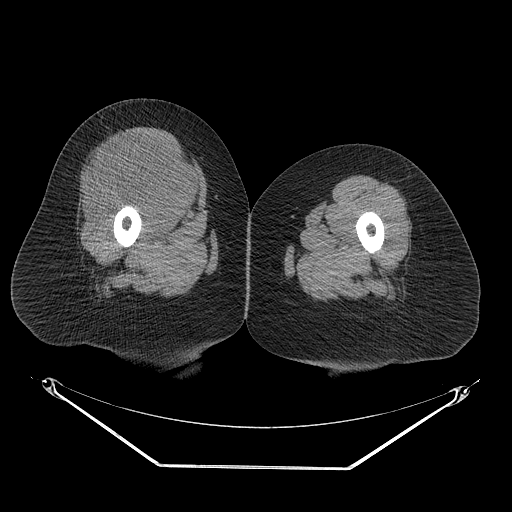
CT of an extremity soft-tissue mass (from a PET/CT study), one axial slice. Slice 33 of 267 in the series (ordered by position). Reconstruction kernel STANDARD. 140 kVp. Soft-tissue window (W 400 / L 40 HU). 3.75 mm slice thickness. 512 × 512 image matrix. Female patient. From the clinical record (not read from this slice): histological type: malignant solitary fibrous tumor; grade: intermediate; site of the primary tumour: right thigh.
Annotated regions visible in this slice (expert contour drawn on MRI and transferred to this co-registered scan by the dataset authors):
- gross tumour volume including surrounding oedema: bounding box [x1, y1, x2, y2] px = [89, 132, 206, 223]
- gross tumour volume (mass): [96, 132, 204, 220]